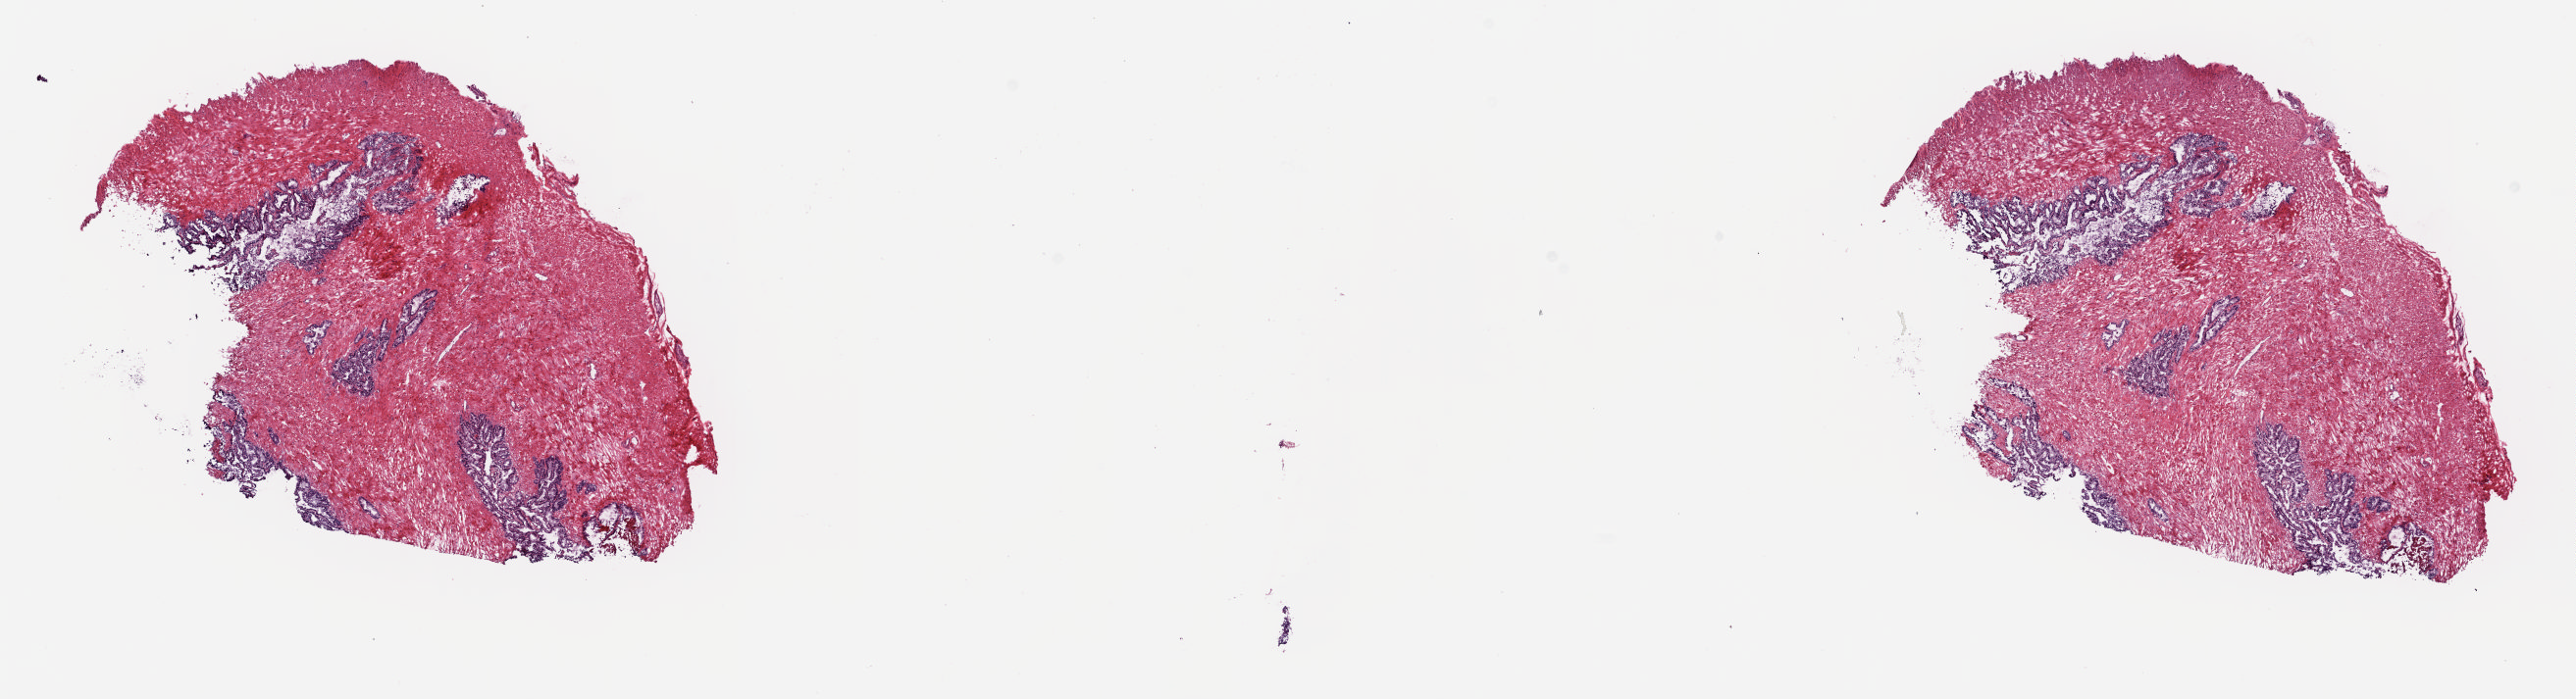
Whole-slide histology image, Hematoxylin and eosin (H&E) stained, low-resolution overview of the scanned area, about 20.8 x 5.7 mm, frozen section from the top of the tissue portion, sample: solid tissue normal (non-tumour tissue), prostate. Male patient; age at initial diagnosis 62 years. Composition of this section per pathologist review: tumour cells 0%, tumour nuclei 0%, normal cells 30%, stromal cells 70%, necrosis 0%. Infiltration values recorded for this section: lymphocyte infiltration 0%, monocyte infiltration 0%, neutrophil infiltration 0%.
* this section: solid tissue normal (non-tumour) sample from the same patient
* patient diagnosis: Adenocarcinoma, NOS (prostate gland)